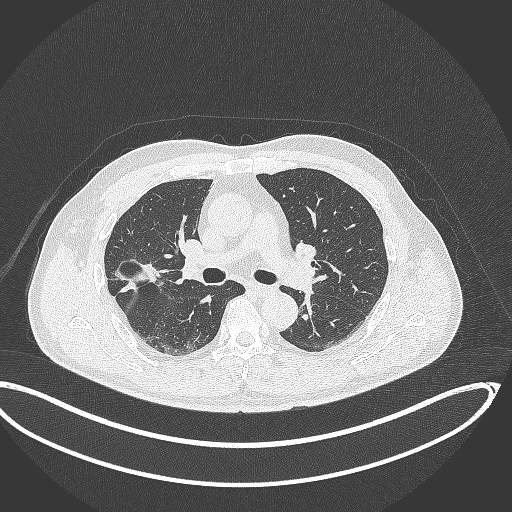
Chest CT, one axial slice; slice 205 of 391 in the series (ordered by position); 120 kVp; lung window (W 1500 / L -600 HU); 1 mm slice thickness; 512 × 512 image matrix, field of view 439 × 439 mm. Patient: male, 63 years. From the clinical record (not read from this slice): clinical TNM (as recorded): T1c N0 M0.
Structures marked on this image (rectangle marked by the reading radiologist):
- lung tumour (recorded histology: adenocarcinoma): box from (x=112, y=256) to (x=165, y=296) px